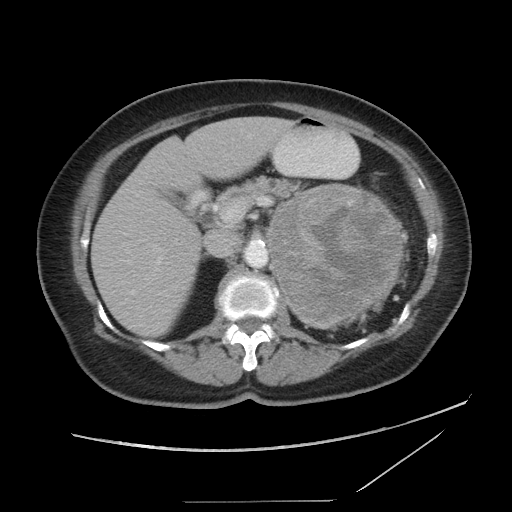
Contrast-enhanced abdominal CT, one axial slice; position 56 of 86 along the scan axis; reconstruction kernel STANDARD; 120 kVp; intravenous contrast given; soft-tissue window (W 400 / L 40 HU); 5 mm slice thickness; 512 × 512 image matrix, field of view 398 × 398 mm. Patient: female, 77 years. Case-level facts recorded for this patient, not image findings: diagnosis: adrenocortical carcinoma; tumour side: left adrenal; tumour size at pathology: 13.1 cm; Ki-67 index: 10 %; stage (as recorded): 3.
Structures marked on this image (semi-automatic segmentation, software-assisted and operator-edited):
- mass: box from (x=266, y=186) to (x=401, y=328) px